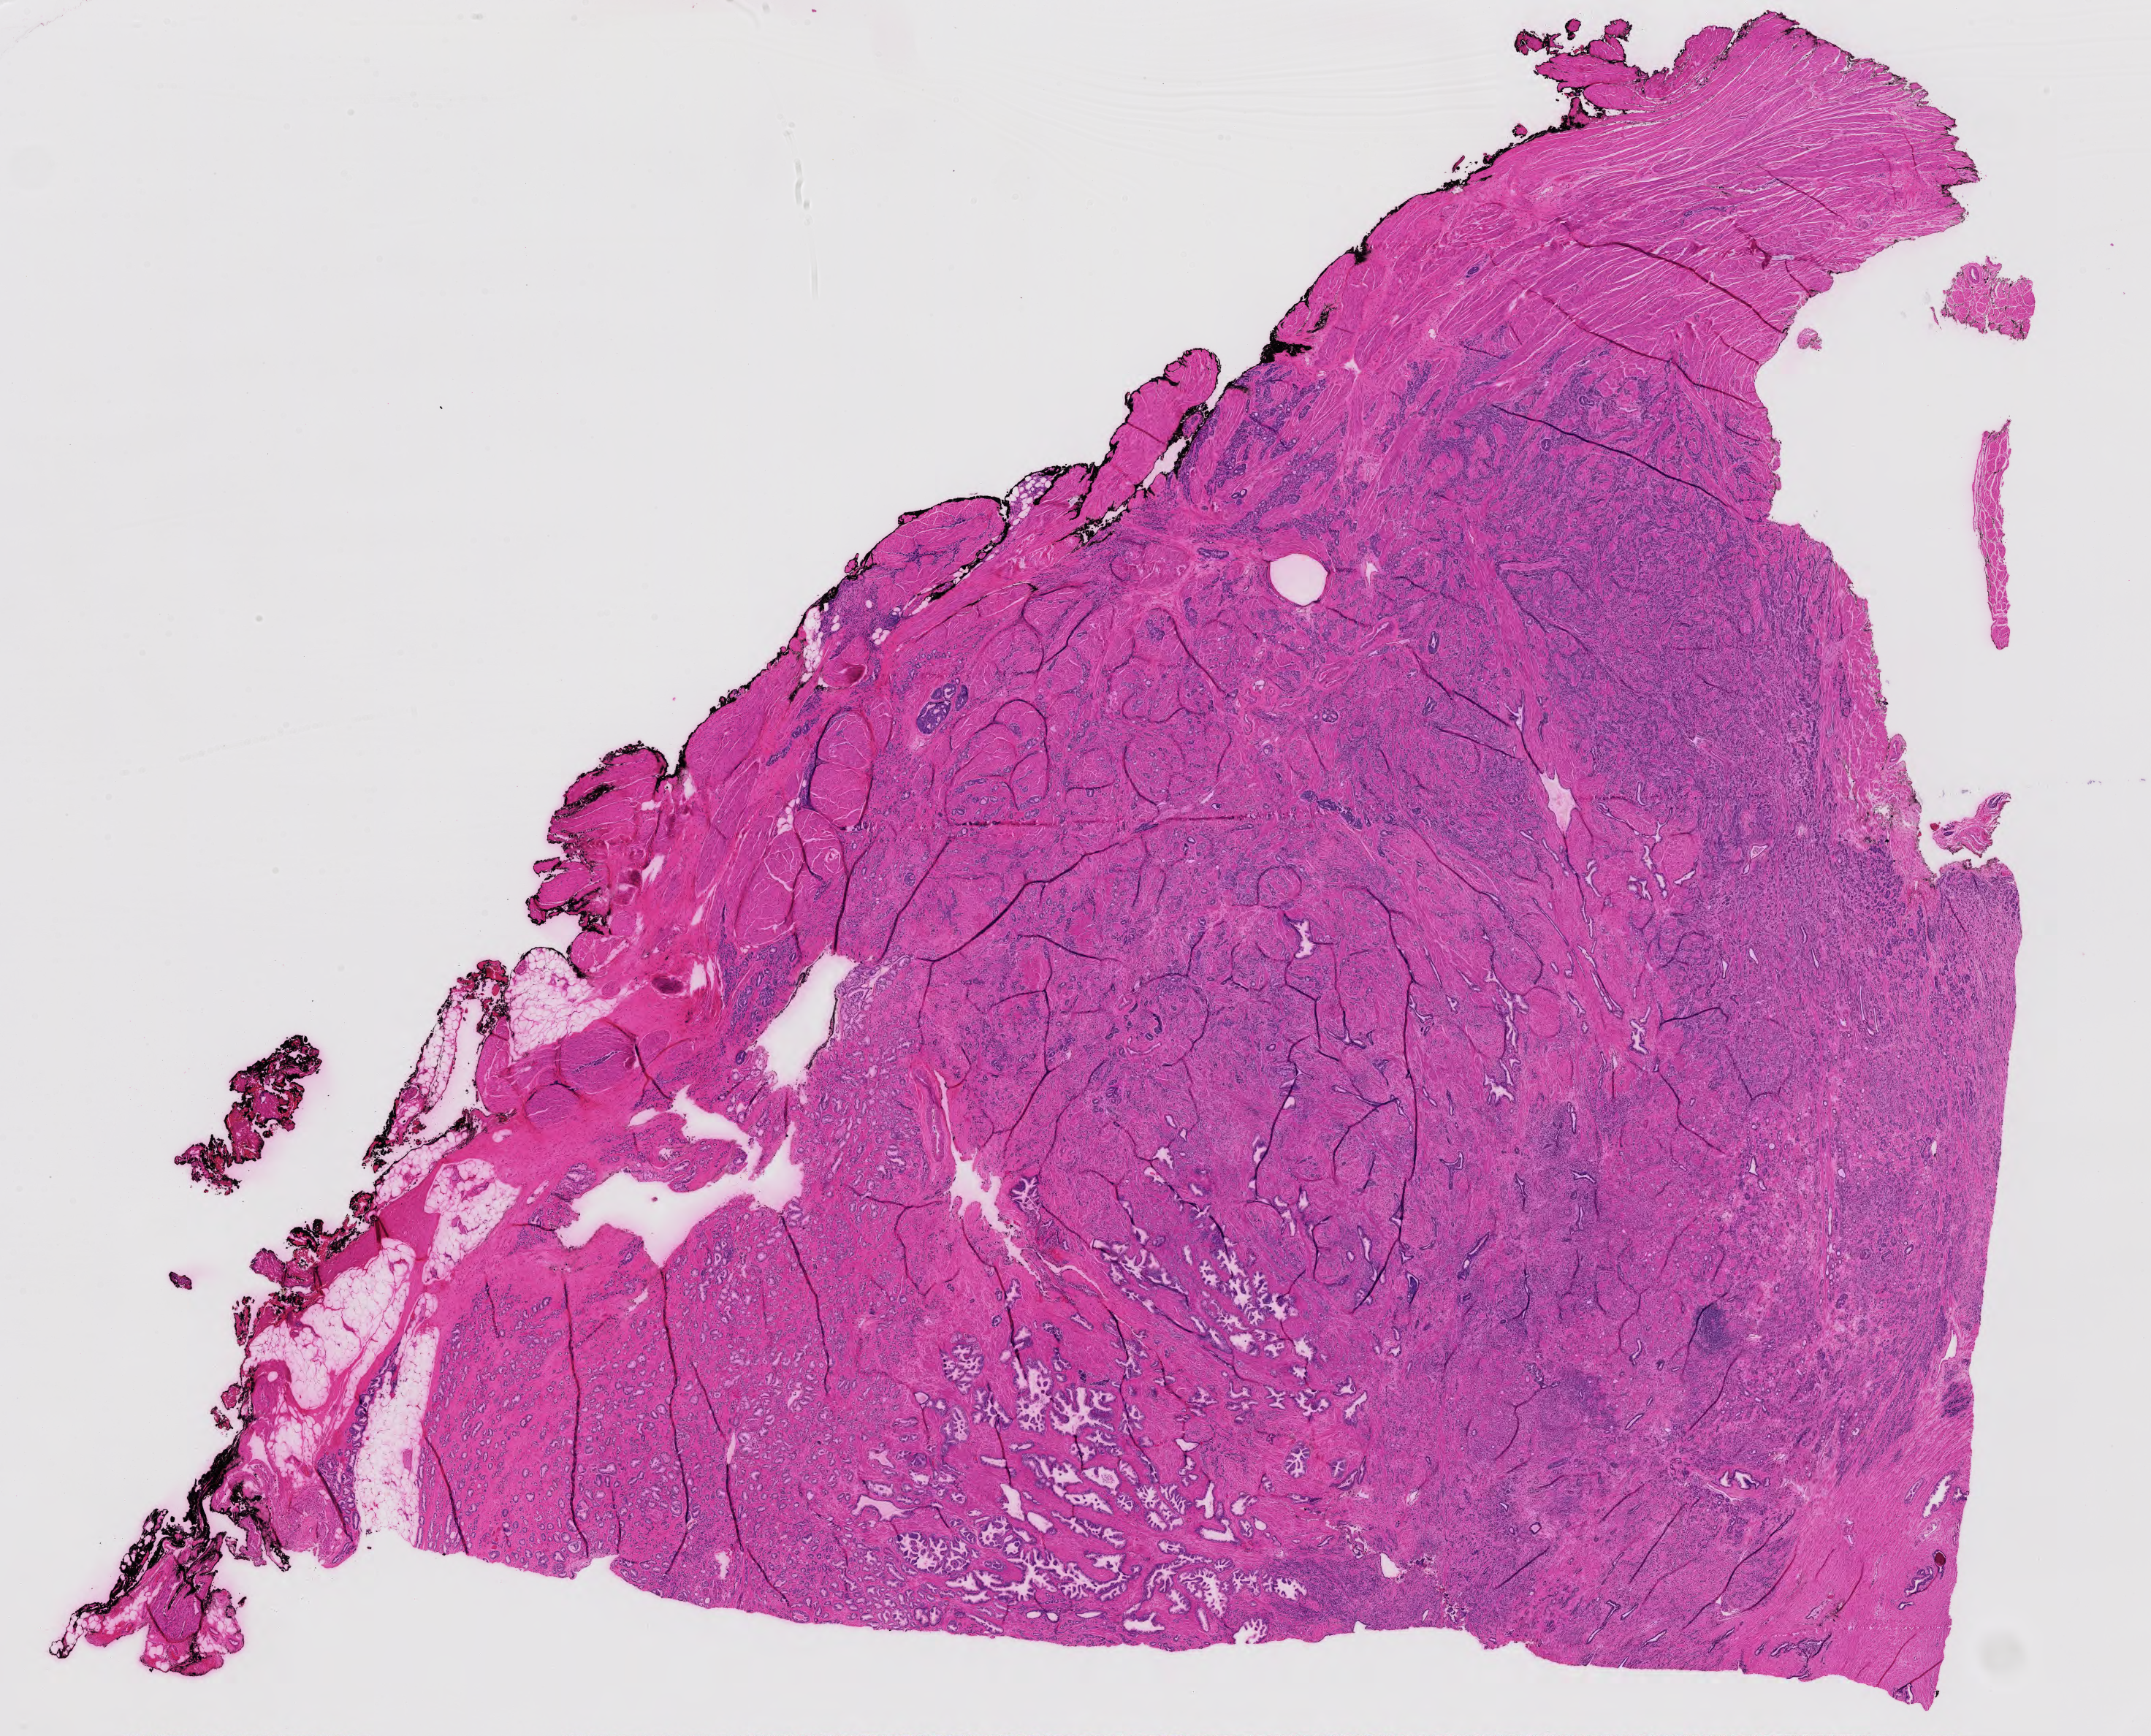
Whole-slide histology image, H&E-stained — shown as a low-resolution overview of the whole scanned area (about 21.4 x 17.2 mm). Formalin-fixed paraffin-embedded (FFPE) diagnostic section. Prostate, primary tumour sample. Male, age 67 years at initial diagnosis.
Diagnosis: Adenocarcinoma, NOS (prostate gland).